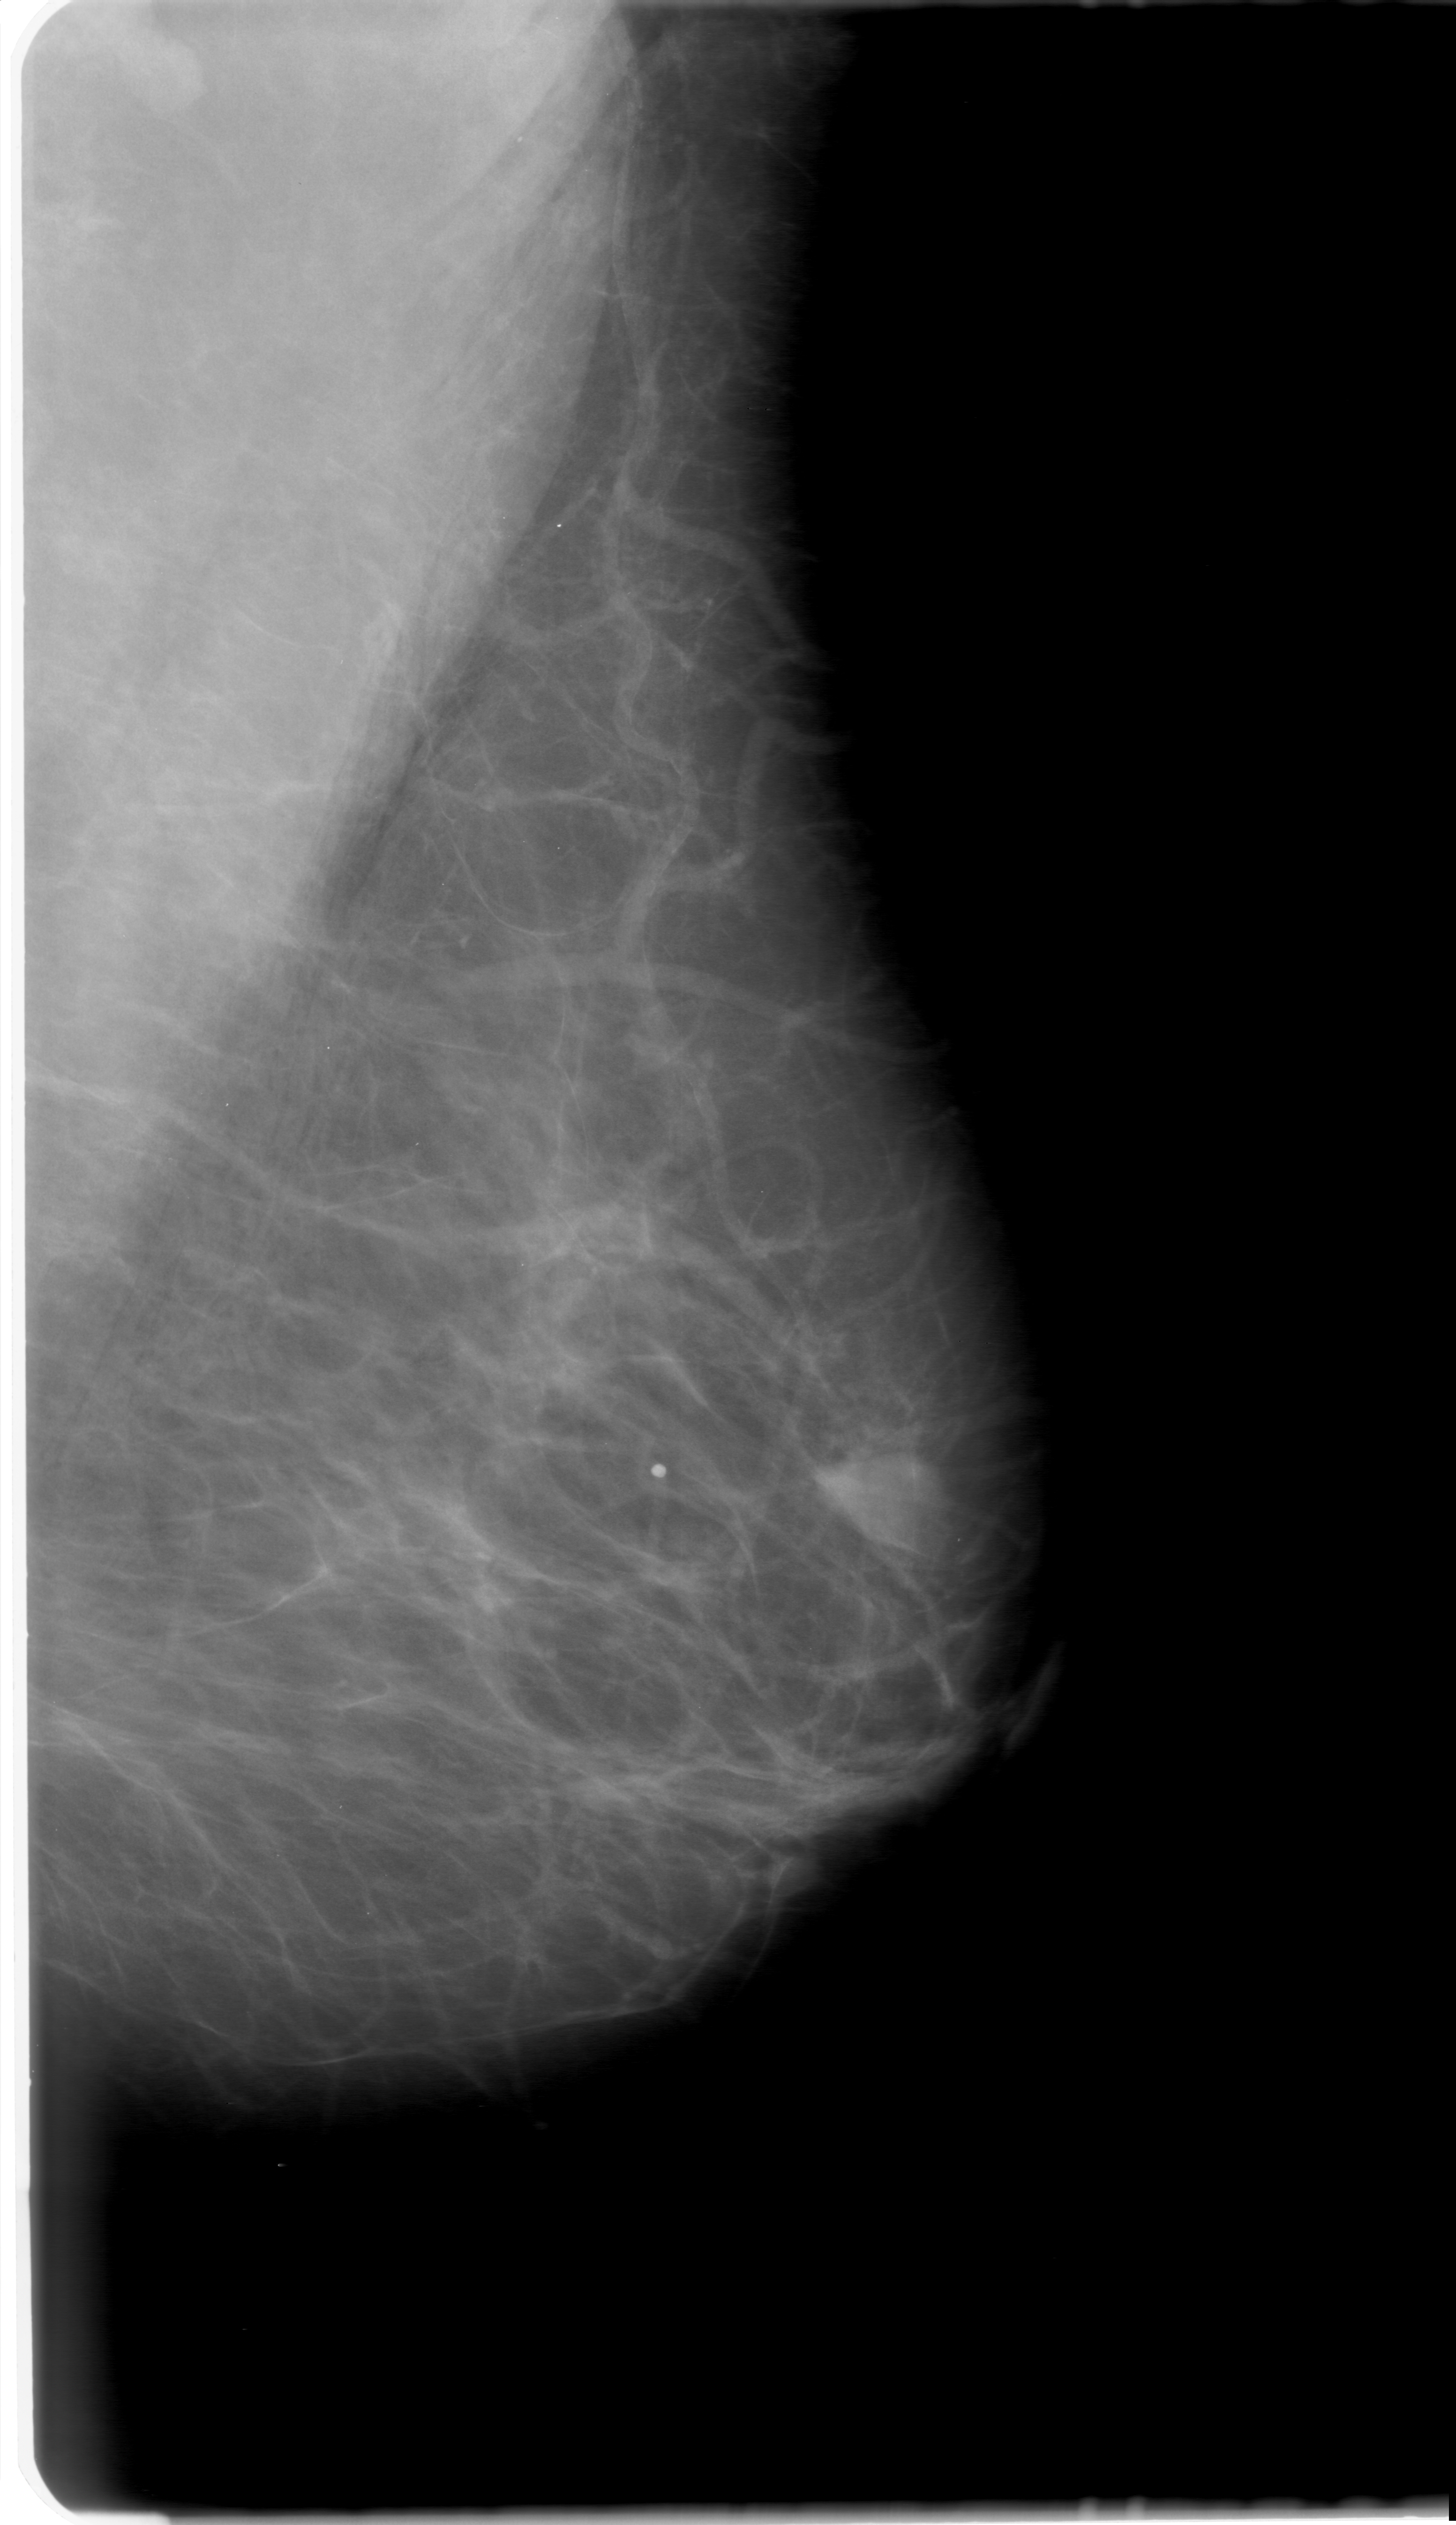
Scanned film-screen mammogram; left breast; mediolateral oblique (MLO) view; 1456 × 2525 image matrix.
Expert-marked regions of interest on this film, with their recorded descriptors:
- mass, shape lobulated, margins obscured; BI-RADS assessment category 0; subtlety rating 5 on a 1 (subtle) to 5 (obvious) scale; pathology (as recorded): benign: bounding box [x1, y1, x2, y2] px = [796, 1415, 981, 1600]